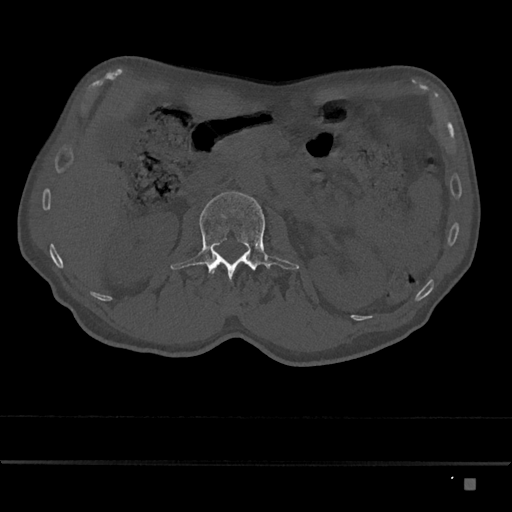
CT including the spine, one axial slice. Position 483 of 797 along the scan axis. Reconstruction kernel Br40s/3. Bone window (W 1800 / L 400 HU). 0.5 mm slice thickness. 512 × 512 image matrix. Patient: male, 72 years. From the clinical record (not read from this slice): primary cancer: prostate.
Annotated regions visible in this slice (semi-automatic segmentation, software-assisted and operator-edited):
- L1 vertebra: bounding box (x1, y1, x2, y2) in pixels: (210, 271, 213, 273)
- L2 vertebra: (170, 191, 299, 281)